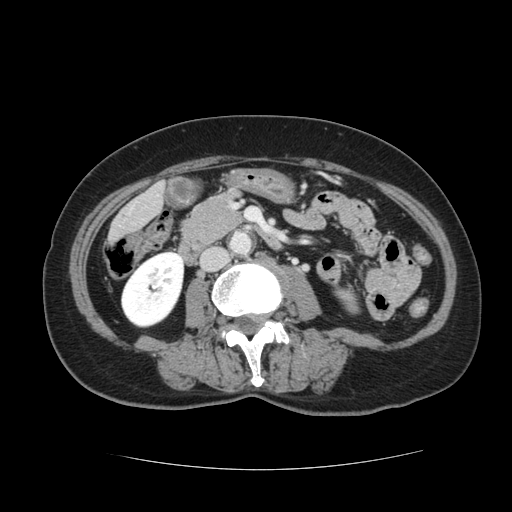
Contrast-enhanced abdominal CT, one axial slice. Slice 21 of 128 in the series (ordered by position). 120 kVp. Intravenous contrast given. Soft-tissue window (W 400 / L 40 HU). 2.5 mm slice thickness. 512 × 512 image matrix, field of view 366 × 366 mm. Female patient, age 67 years. From the clinical record (not read from this slice): diagnosis: colorectal cancer liver metastases, imaged before liver resection; multiple liver metastases: yes; largest metastasis: 3 cm; disease in both lobes: yes.
Structures marked on this image (expert manual segmentation):
- liver: bounding box (x1, y1, x2, y2) in pixels: (112, 186, 163, 240)
- planned liver remnant (the part of the liver to remain after resection): (111, 207, 142, 240)